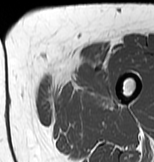
MRI of an extremity soft-tissue mass, one axial slice. Position 13 of 83 along the scan axis. MR volume resampled by the dataset authors to the PET/CT grid (not the native acquisition matrix). 3.27 mm slice thickness. 154 × 162 image matrix, field of view 150 × 158 mm. Female patient. From the clinical record (not read from this slice): histological type: myxofibrosarcoma; grade: intermediate; site of the primary tumour: left thigh.
Structures marked on this image (expert contour drawn on MRI and transferred to this co-registered scan by the dataset authors):
- gross tumour volume including surrounding oedema: bounding box (x1, y1, x2, y2) in pixels: (40, 66, 114, 108)
- gross tumour volume (mass): (81, 68, 95, 74)